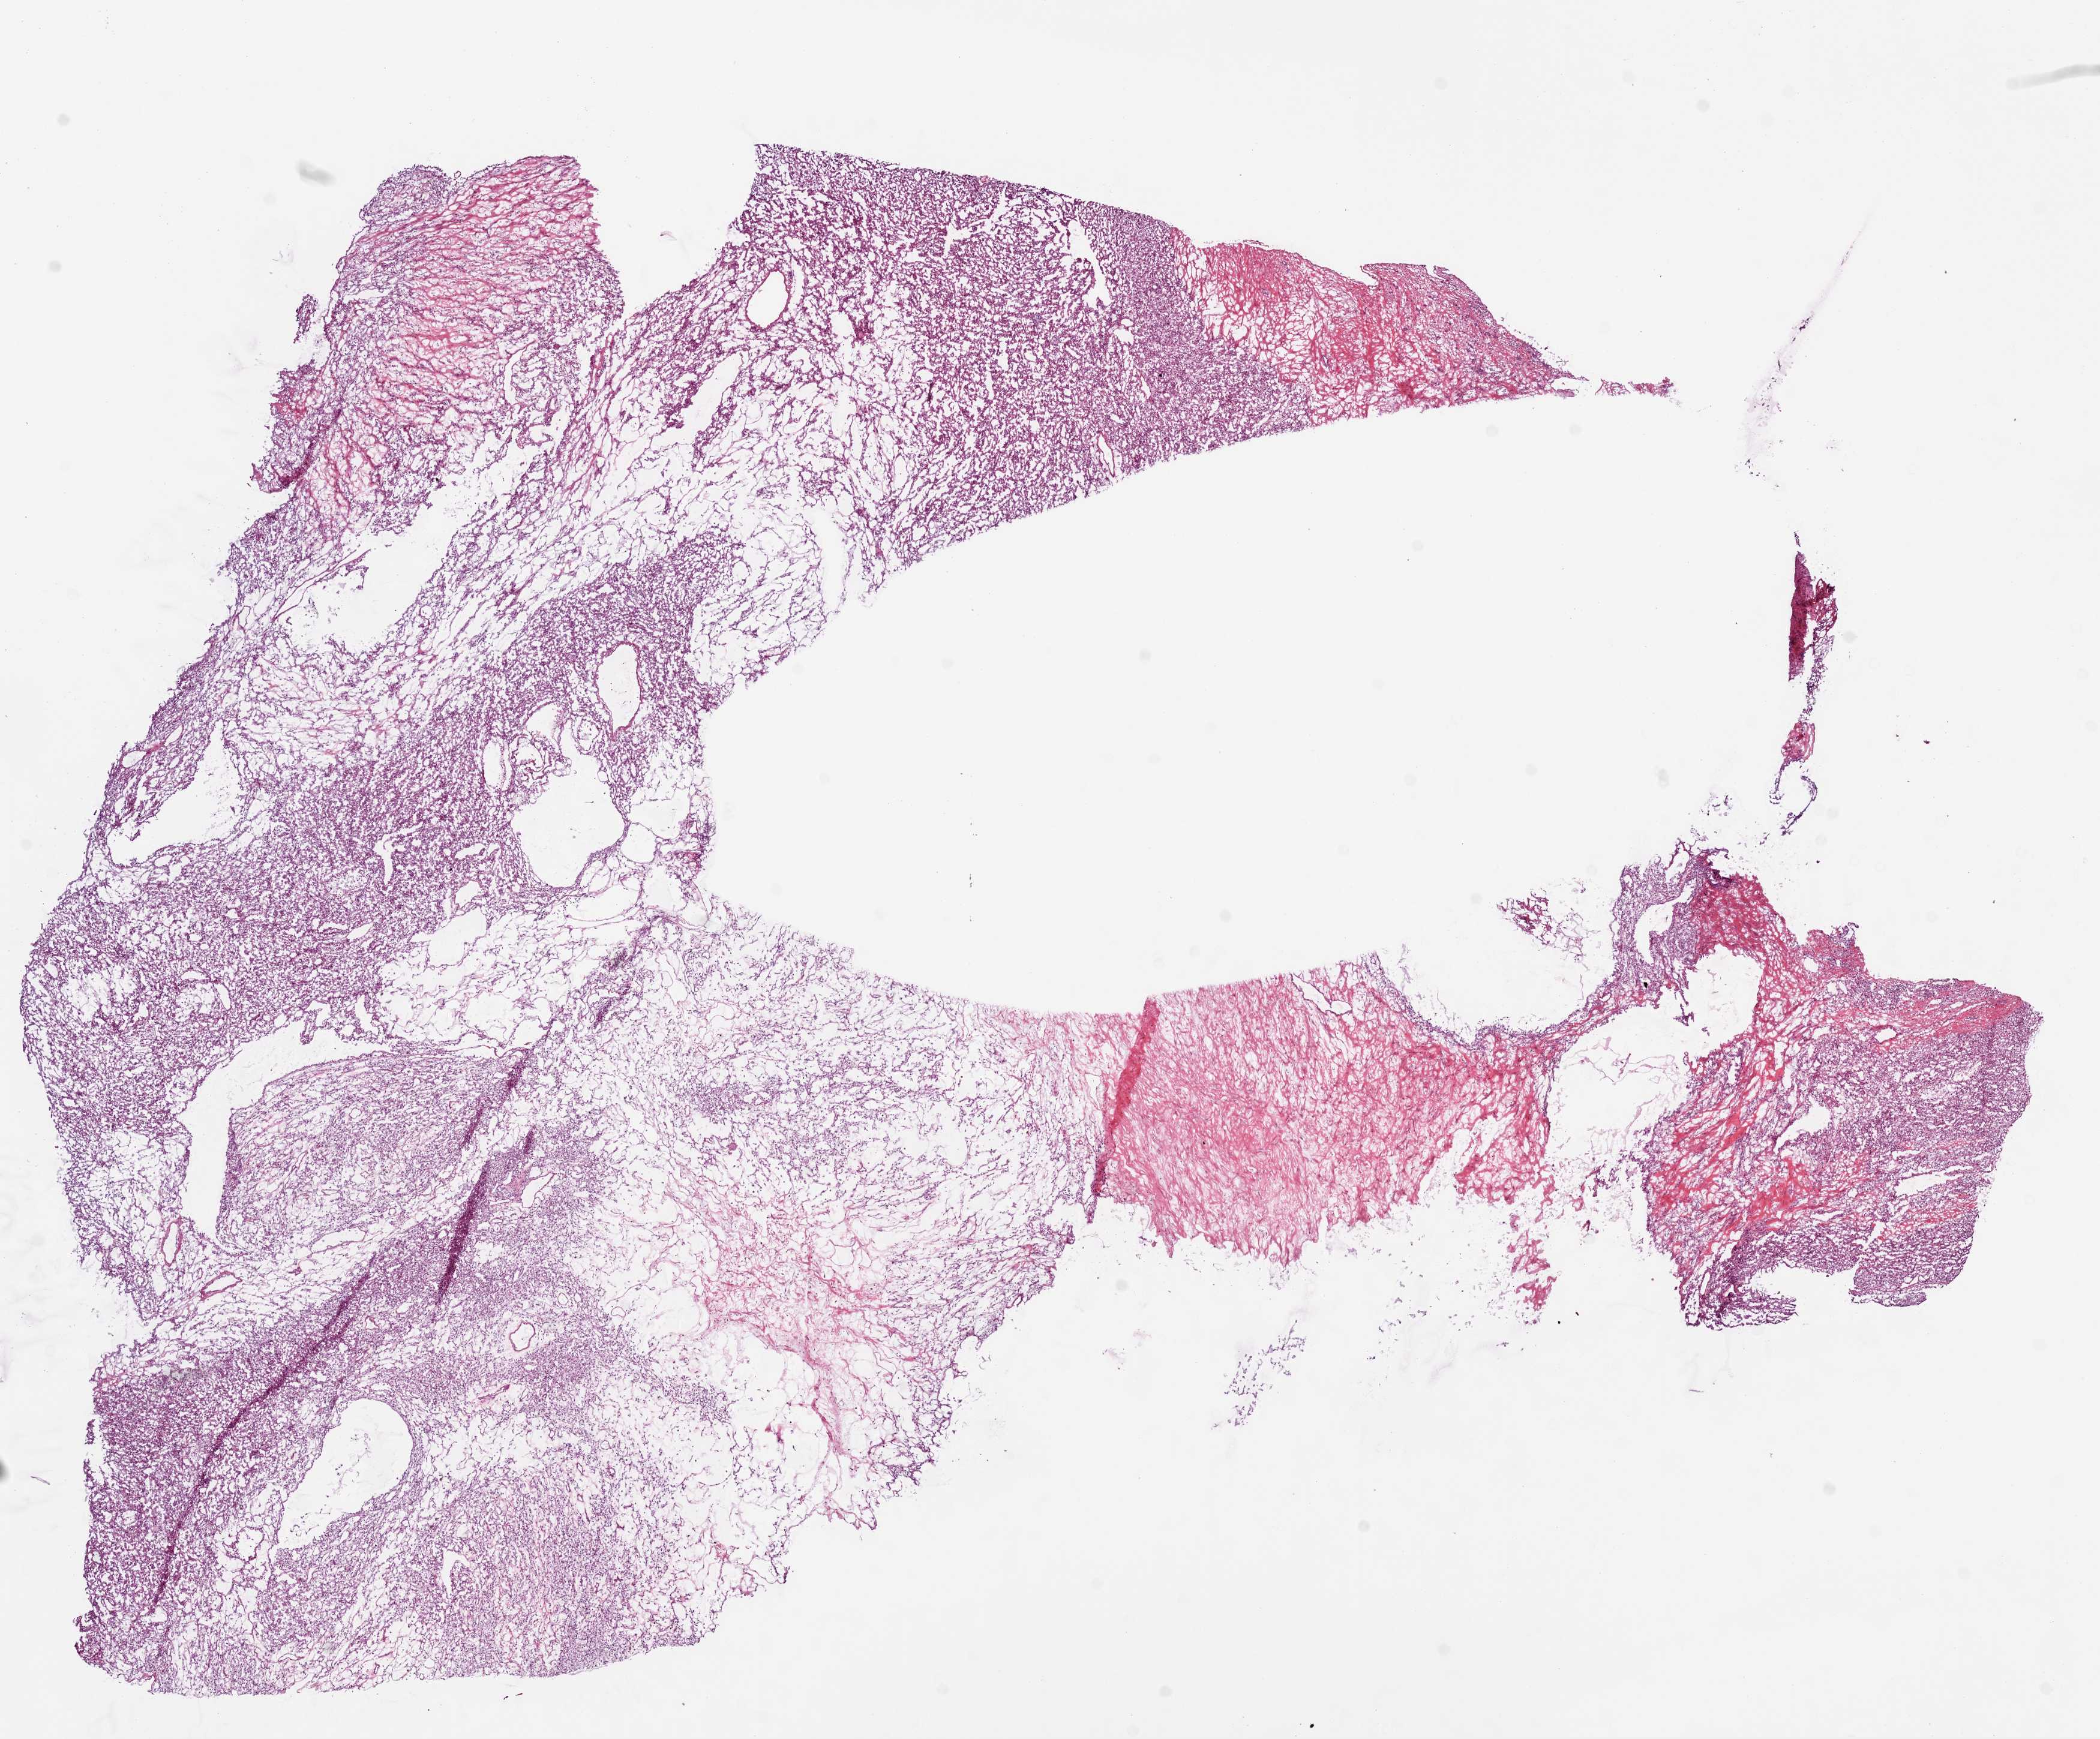
H&E whole-slide image — shown as a low-resolution overview of the whole scanned area (about 14.0 x 11.6 mm, acquisition: 20x scan), frozen section from the bottom of the tissue portion, sample: primary tumour, kidney. Male, age 44 years at initial diagnosis. Histologic grade: G3 (poorly differentiated). Composition of this section per pathologist review: tumour cells 90%, tumour nuclei 80%, normal cells 0%, stromal cells 10%, necrosis 0%.
• histologic diagnosis: Clear cell adenocarcinoma, NOS
• AJCC pathologic stage: III
• laterality: right